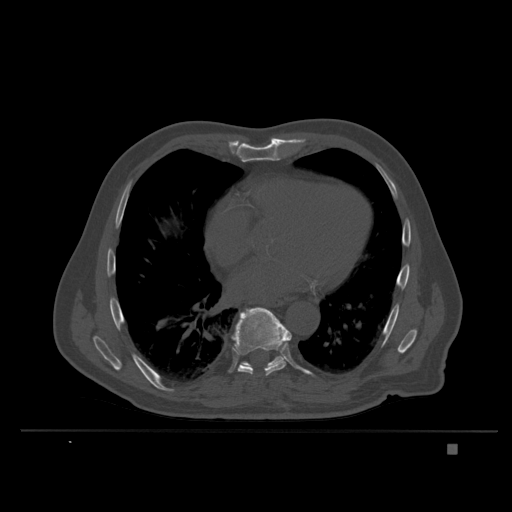
CT including the spine, one axial slice; slice 225 of 435 in the series (ordered by position); bone window (W 1800 / L 400 HU); 1.5 mm slice thickness; 512 × 512 image matrix, field of view 434 × 434 mm. Male patient, age 73 years. From the clinical record (not read from this slice): primary cancer: skin.
Structures marked on this image (semi-automatic segmentation, software-assisted and operator-edited):
- T8 vertebra: box from (x=231, y=307) to (x=292, y=376) px
- T9 vertebra: (x=240, y=308)–(x=284, y=368)